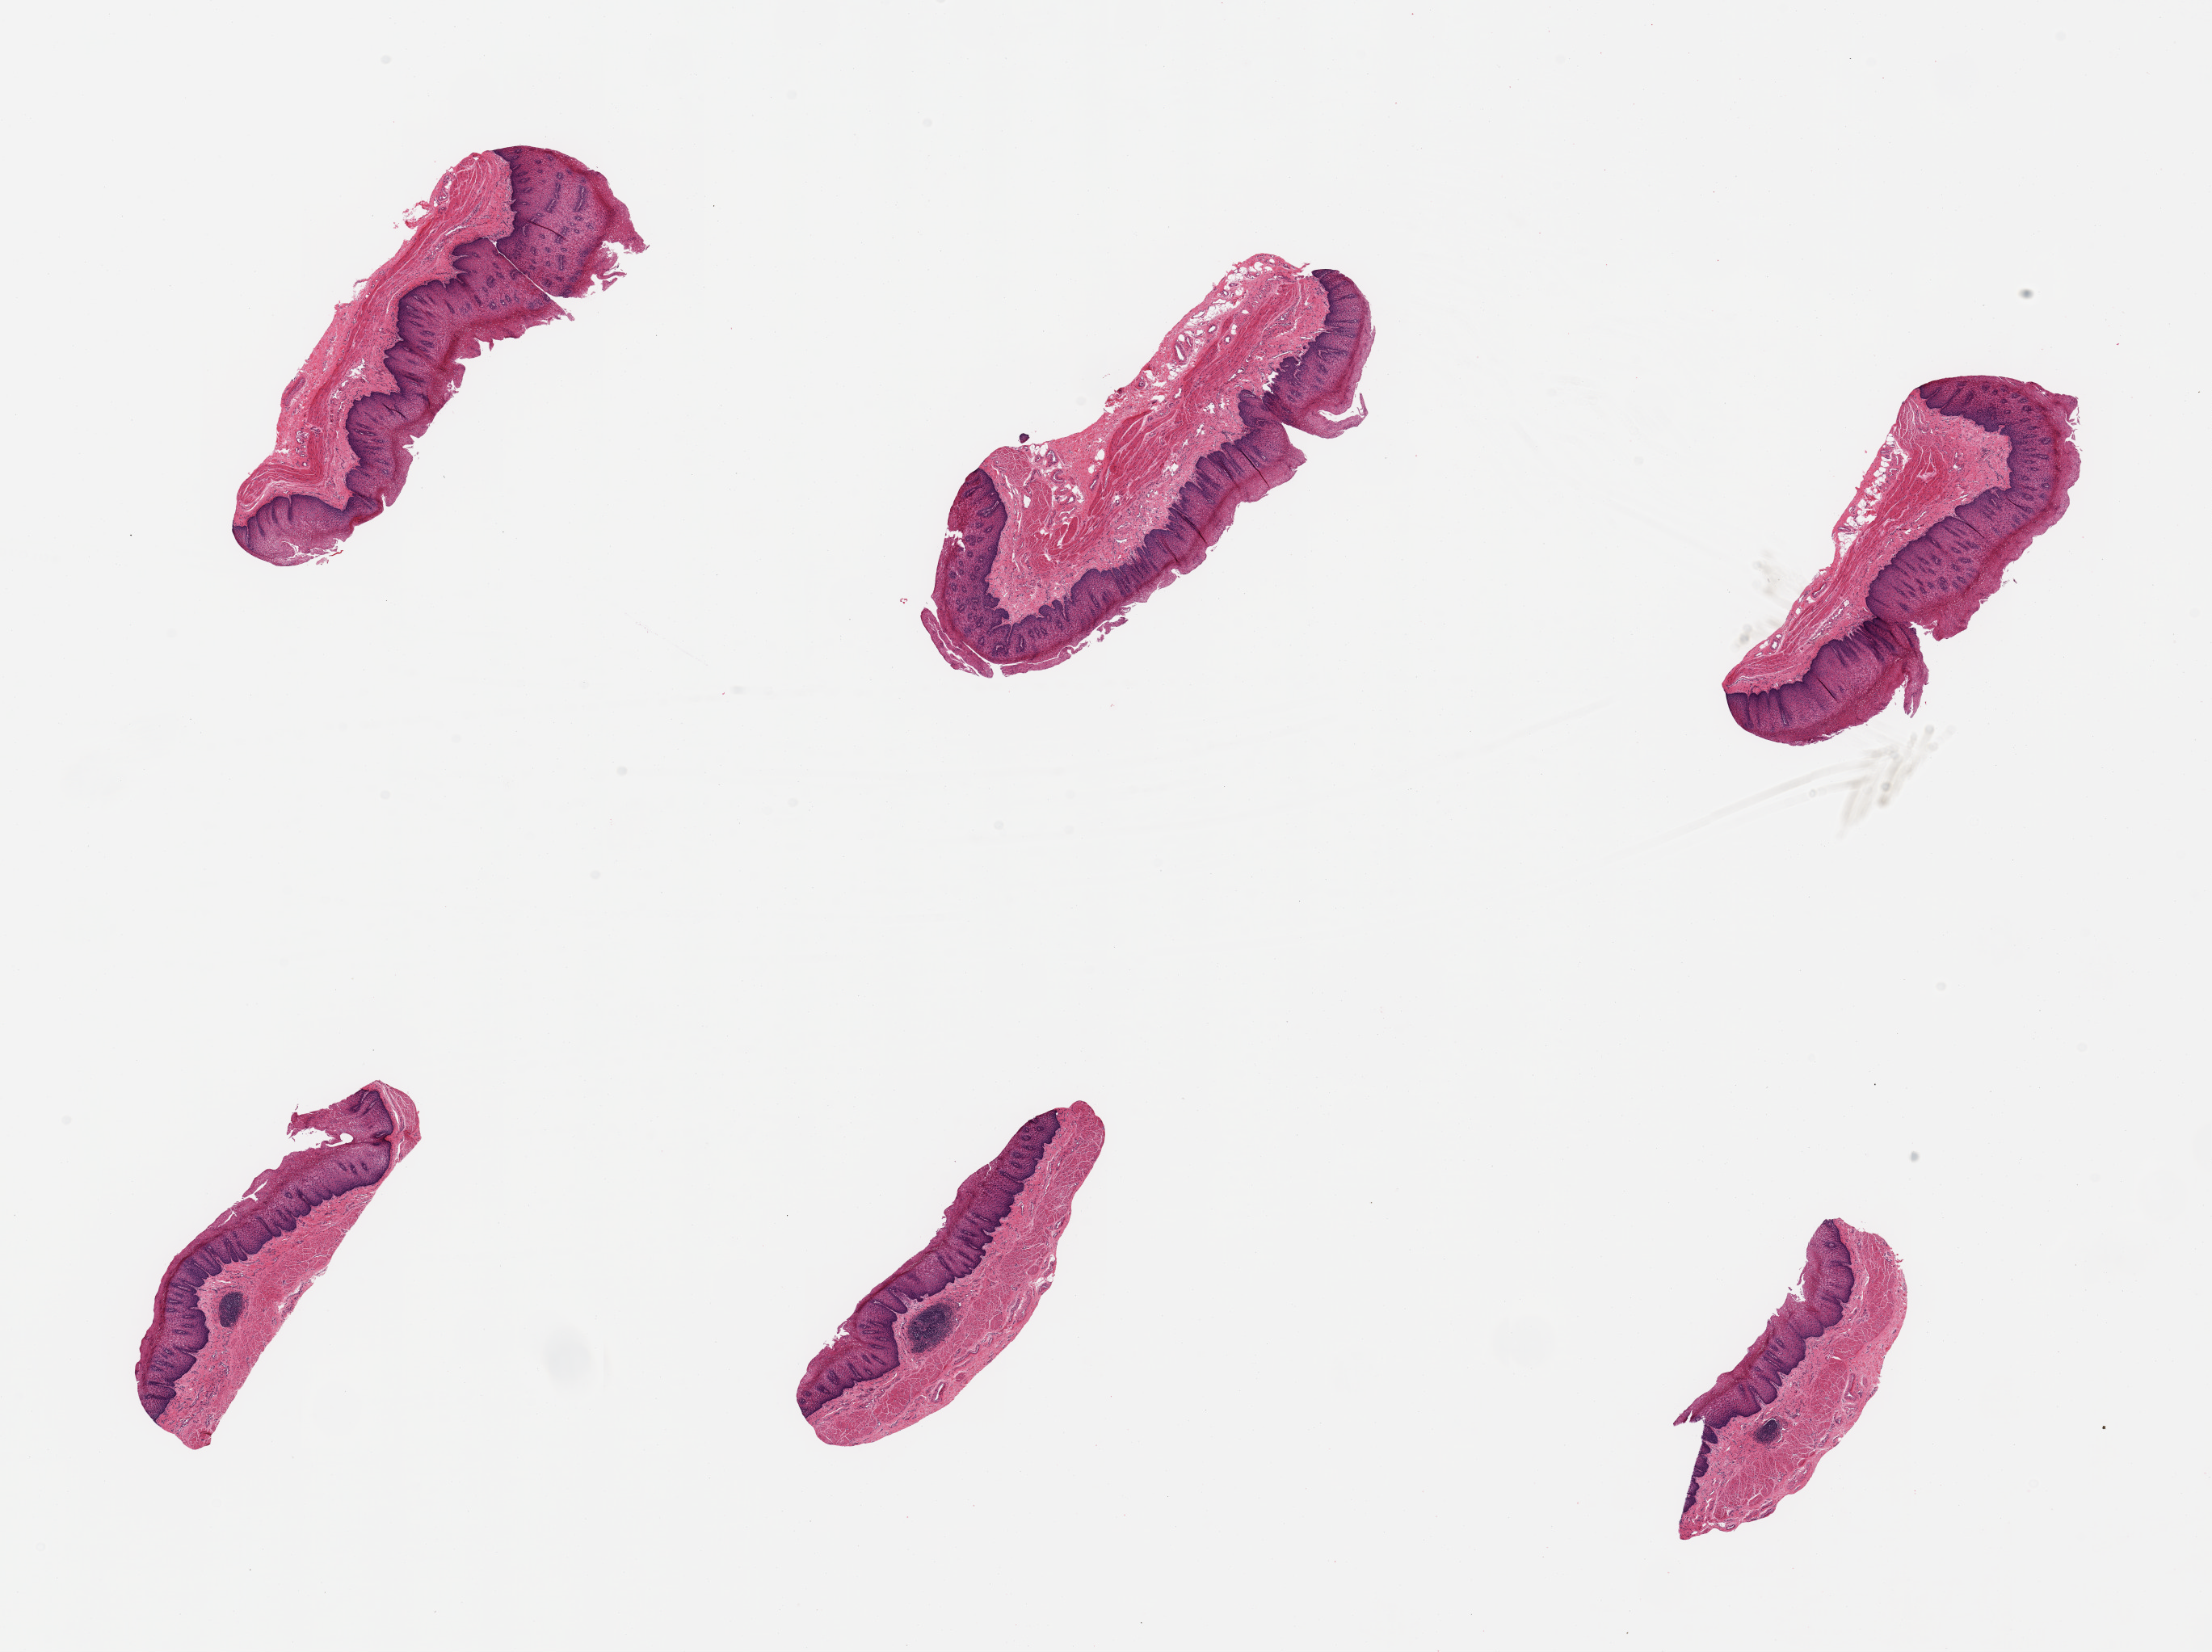
Whole-slide image, haematoxylin and eosin stain, brightfield — low-resolution overview of the scanned area, about 21.7 x 16.2 mm (slide scanned at 20x).
Specimen: PAXgene-fixed paraffin-embedded (PFPE) section; sampled site (target tissue): gastroesophageal junction; tissue donor sample.